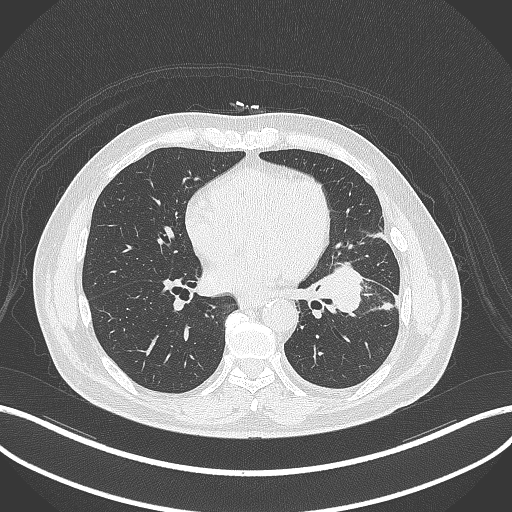
Chest CT, one axial slice. Position 155 of 230 along the scan axis. Reconstruction kernel B70f. Lung window (W 1500 / L -600 HU). 512 × 512 image matrix, field of view 400 × 400 mm. Male patient, age 68 years. From the clinical record (not read from this slice): clinical TNM (as recorded): T2b N0 M0.
Structures marked on this image (bounding box drawn by a radiologist):
- lung tumour (recorded histology: squamous cell carcinoma): bounding box <311,257,365,315> (left, top, right, bottom; pixels)